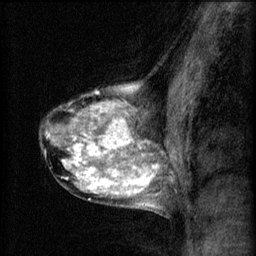
Breast MRI (dynamic contrast-enhanced), one sagittal slice. Slice 40 of 60 in the series (ordered by position). 3 images stored at this slice position (order not interpretable as contrast timing). 1.5 T. TE 4.2 ms, TR 8.2 ms. 2 mm slice thickness. 256 × 256 image matrix. Female patient, age 40 years.
Outlined on this slice (semi-automatic segmentation, software-assisted and operator-edited):
- analysis volume of interest (the breast-tissue region the enhancement analysis was run in; not a lesion): bounding box (x1, y1, x2, y2) in pixels: (39, 80, 167, 211)
- tumour enhancement mask (voxels above the 70 % enhancement threshold inside the analysis volume of interest): (47, 86, 161, 207)